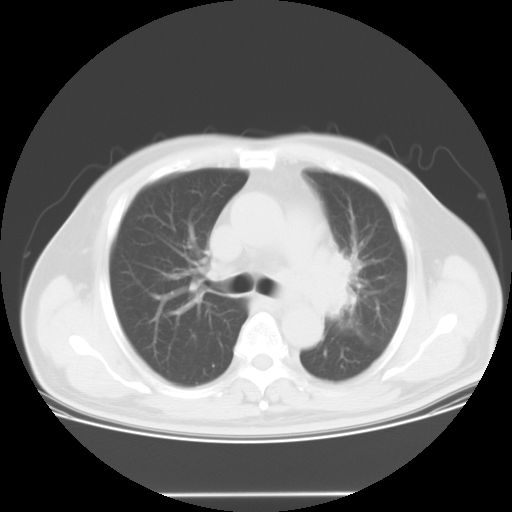
Chest CT, one axial slice; slice 19 of 28 in the series (ordered by position); reconstruction kernel STANDARD; 120 kVp; lung window (W 1500 / L -600 HU); 512 × 512 image matrix, field of view 398 × 398 mm. Male patient, age 61 years. From the clinical record (not read from this slice): clinical TNM (as recorded): T3 N1 M1; histopathological grade: G3.
Annotated regions visible in this slice (rectangle marked by the reading radiologist):
- lung tumour (recorded histology: small cell carcinoma): box from (x=329, y=236) to (x=369, y=331) px